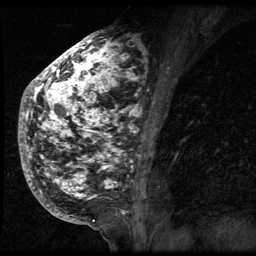
Breast MRI (dynamic contrast-enhanced), one sagittal slice. Position 32 of 64 along the scan axis. 3 images stored at this slice position (order not interpretable as contrast timing). 1.5 T. TE 4.2 ms, TR 9 ms. 2.5 mm slice thickness. 256 × 256 image matrix, field of view 180 × 180 mm. Patient: female, 50 years. From the clinical record (not read from this slice): setting: breast cancer imaged before/during neoadjuvant chemotherapy; receptor status: triple-negative.
Structures marked on this image (semi-automatically segmented with operator editing):
- analysis volume of interest (the breast-tissue region the enhancement analysis was run in; not a lesion): bounding box (x1, y1, x2, y2) in pixels: (24, 39, 140, 212)
- tumour enhancement mask (voxels above the 140 % enhancement threshold inside the analysis volume of interest): (24, 39, 140, 211)